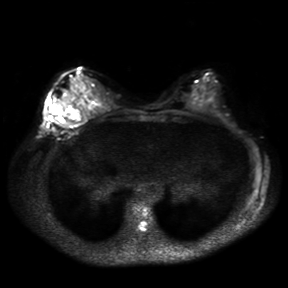
Breast MRI, one axial slice; slice 15 of 30 in the series (ordered by position); diffusion-weighted series; image 2 of 4 stored at this slice position (different b-values; order by instance number); 3 T; 288 × 288 image matrix, field of view 360 × 360 mm. Female patient.
Annotated regions visible in this slice (expert manual segmentation):
- tumour on diffusion-weighted imaging: bounding box [x1, y1, x2, y2] px = [57, 104, 73, 127]